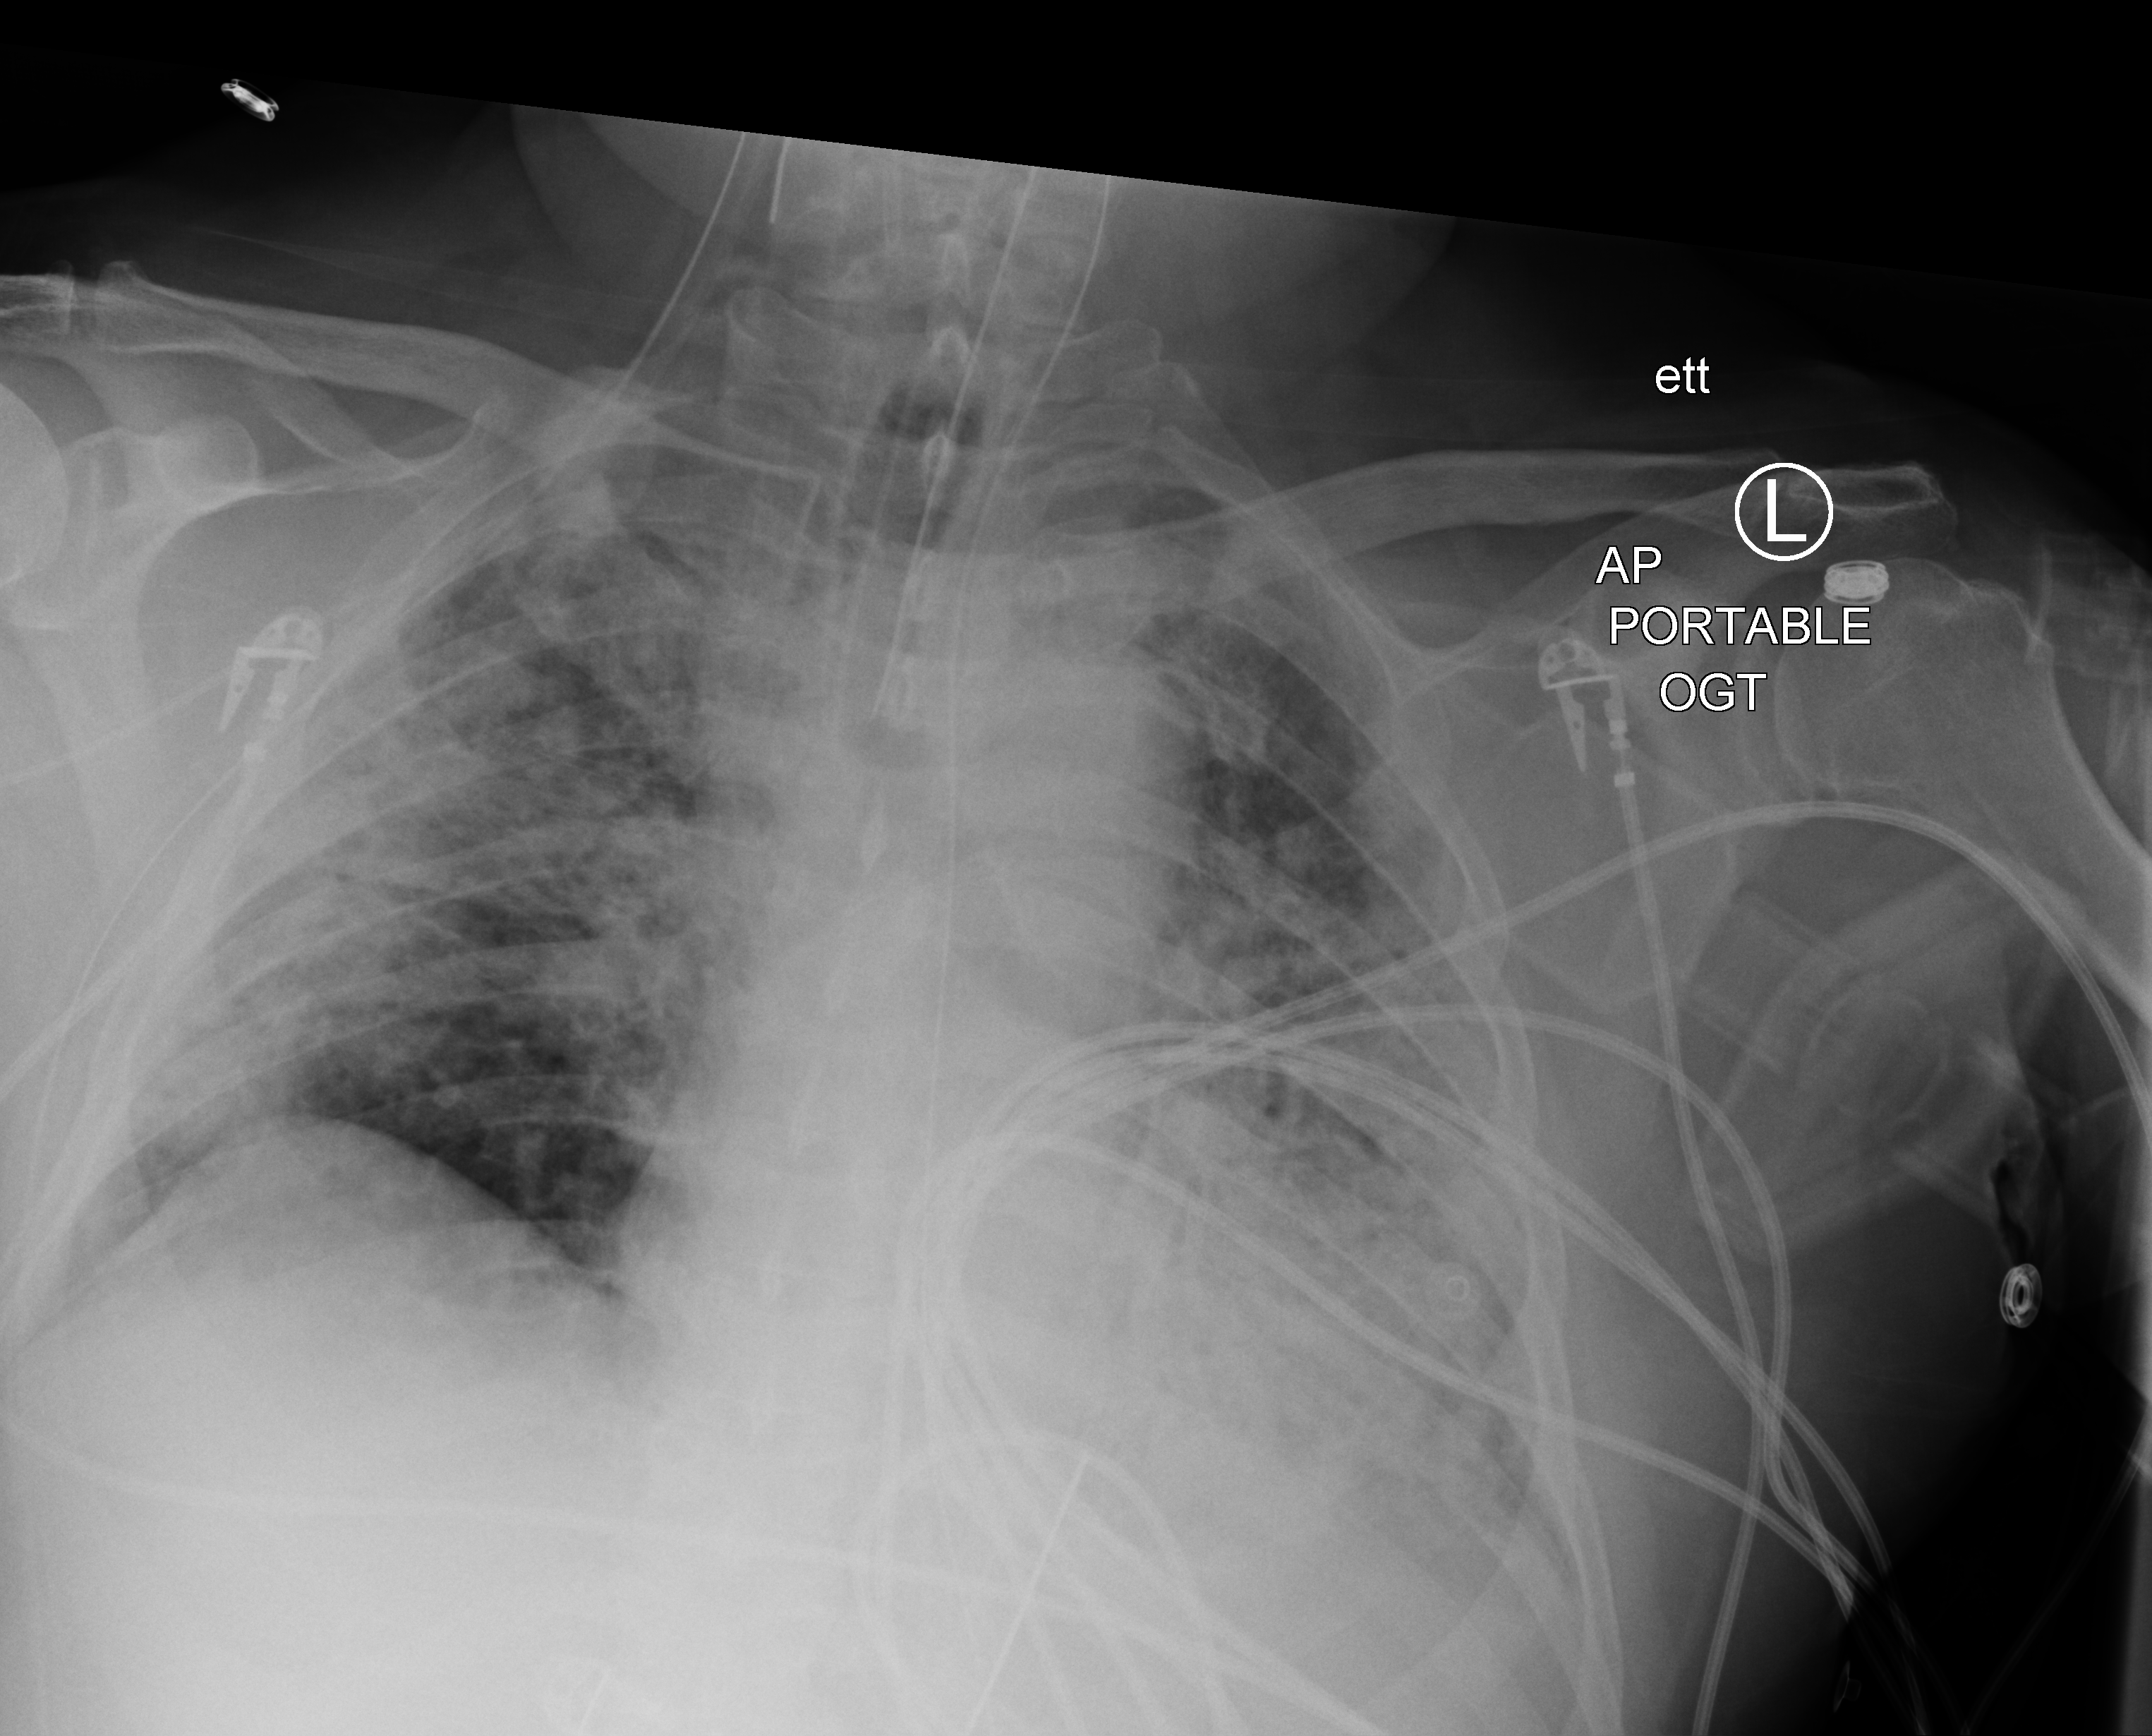
Chest X-ray (portable); anteroposterior (AP) projection. Male patient hospitalised with COVID-19, age 60–74 years.
Hospital-stay facts (about this admission, not read from this image; timing relative to this image not recorded):
- mechanically ventilated during this hospital stay: yes
- diabetes (admission record): yes